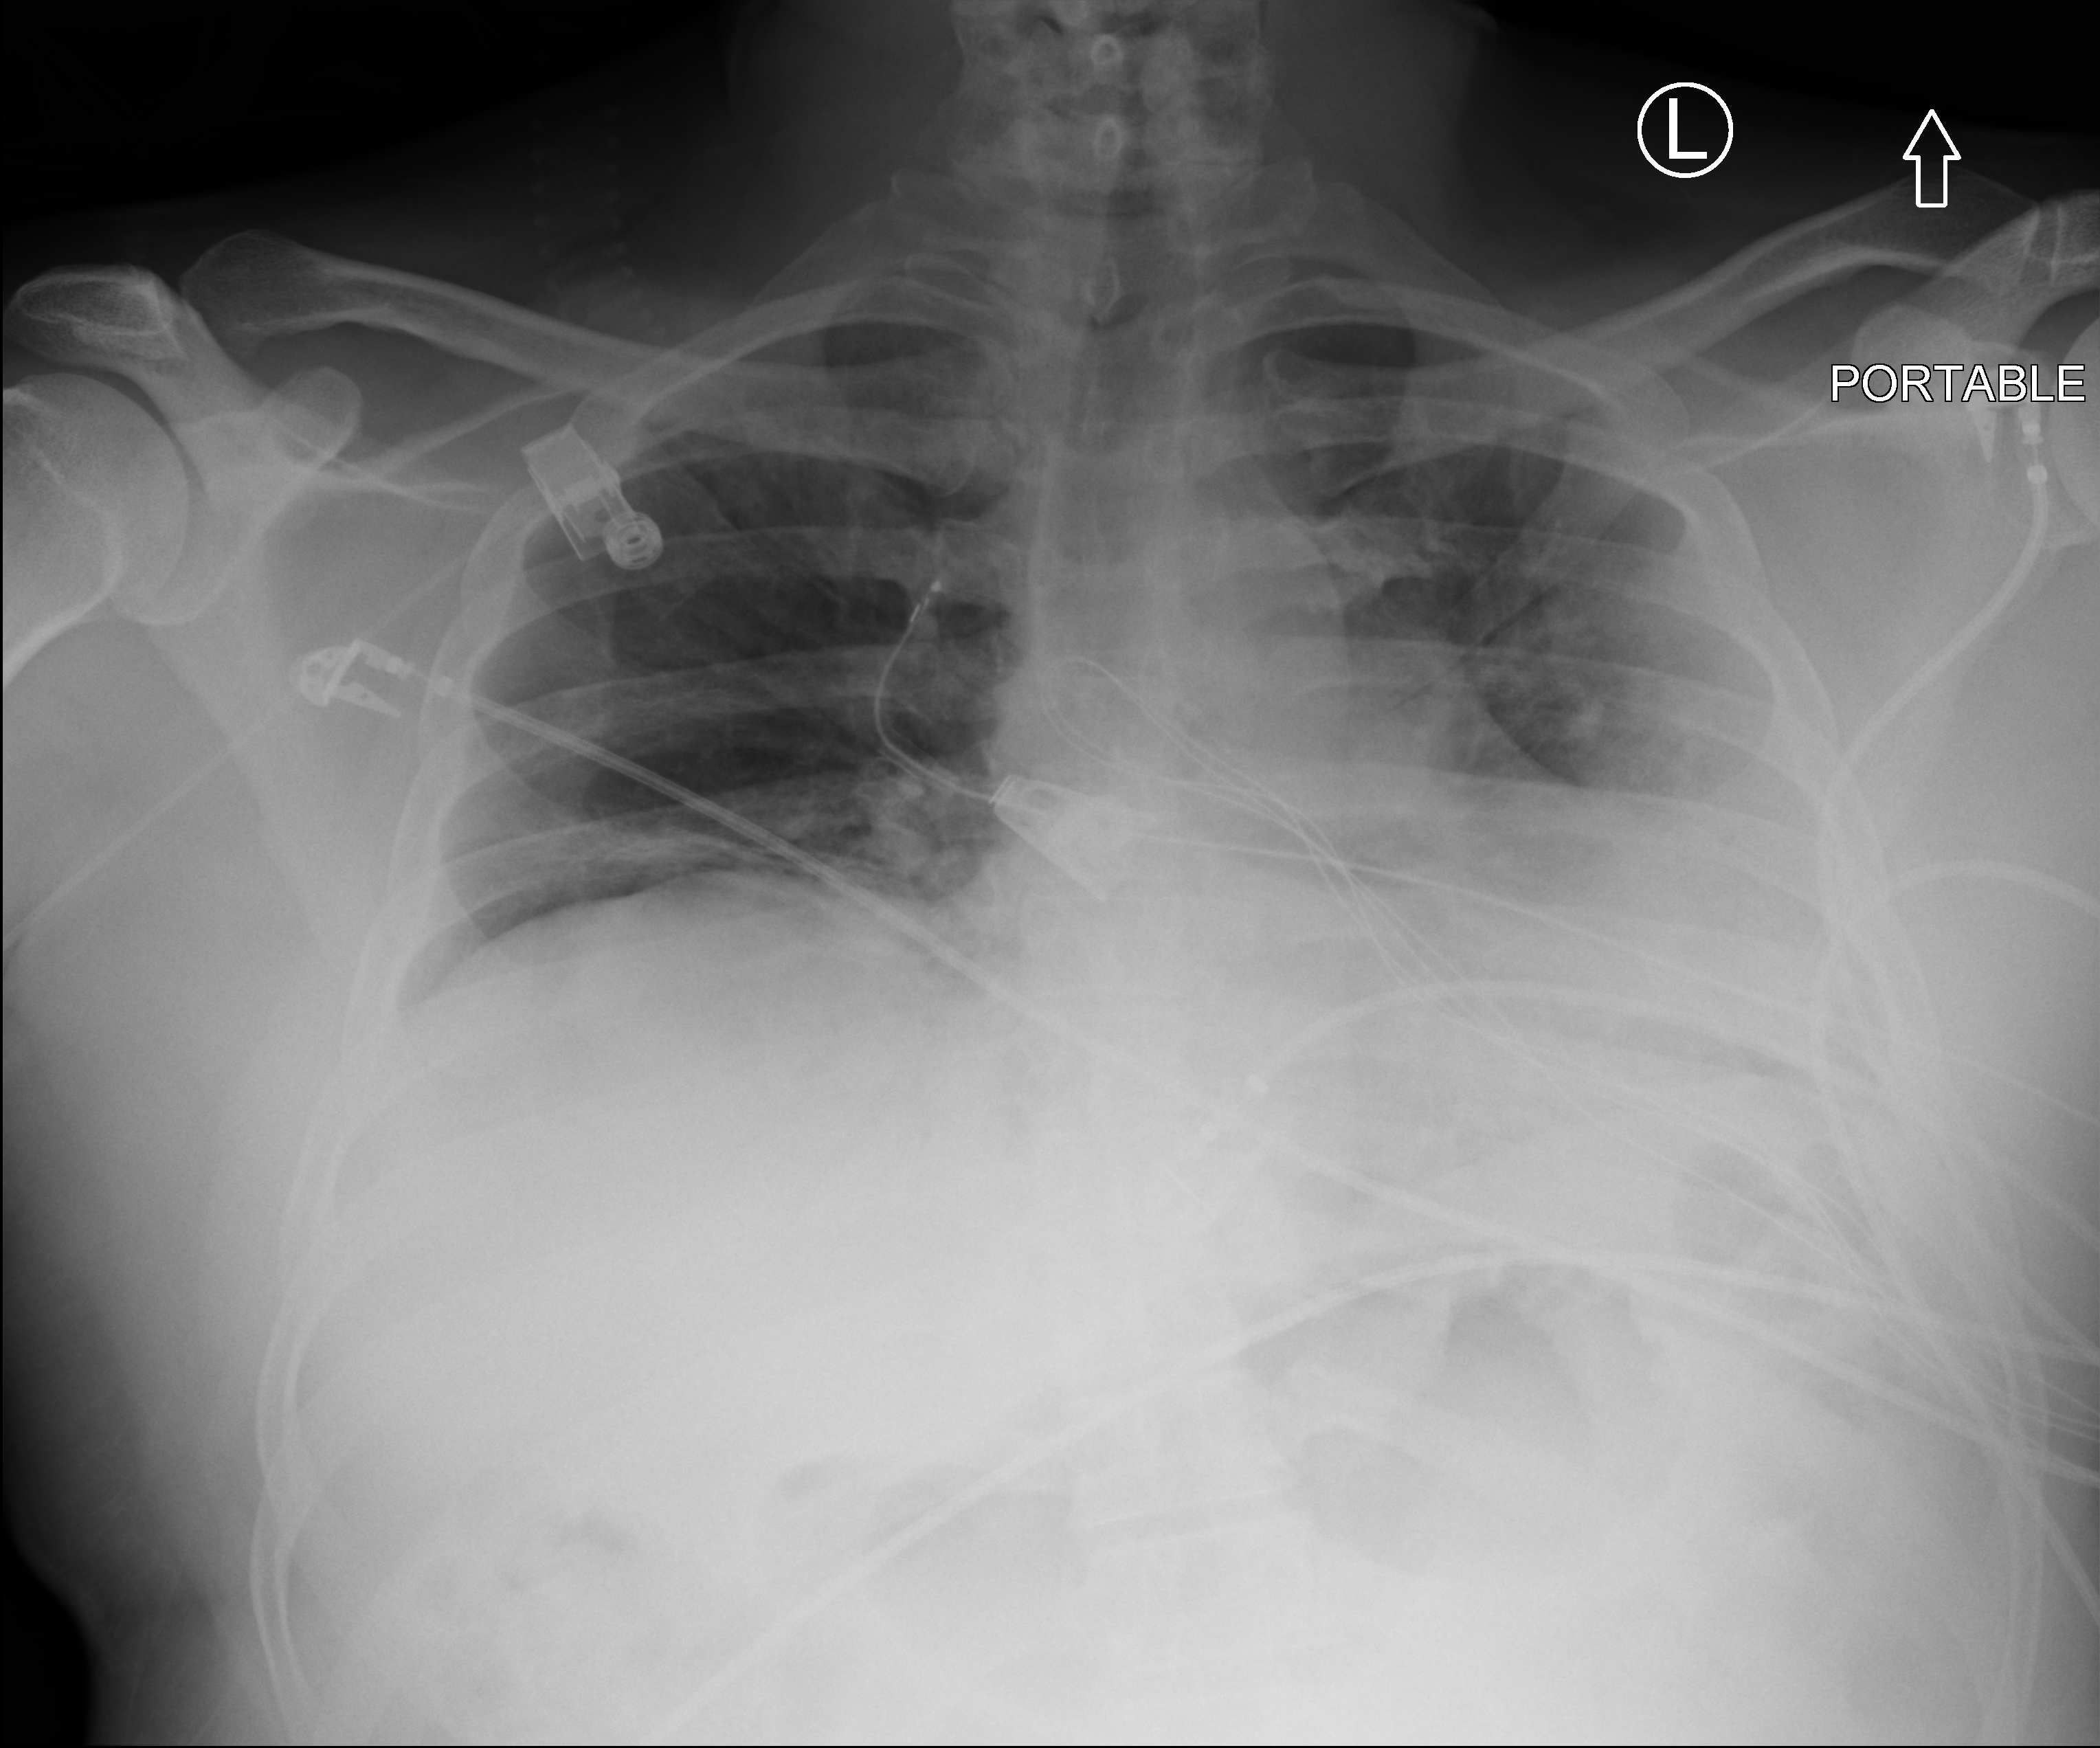
Bedside chest radiograph (computed radiography); anteroposterior (AP) projection. Male patient hospitalised with COVID-19, age 18–59 years.
From the hospital-stay record, not from the radiograph (when in the stay this image was taken is not recorded): admitted to intensive care during this hospital stay: yes; mechanically ventilated during this hospital stay: no.